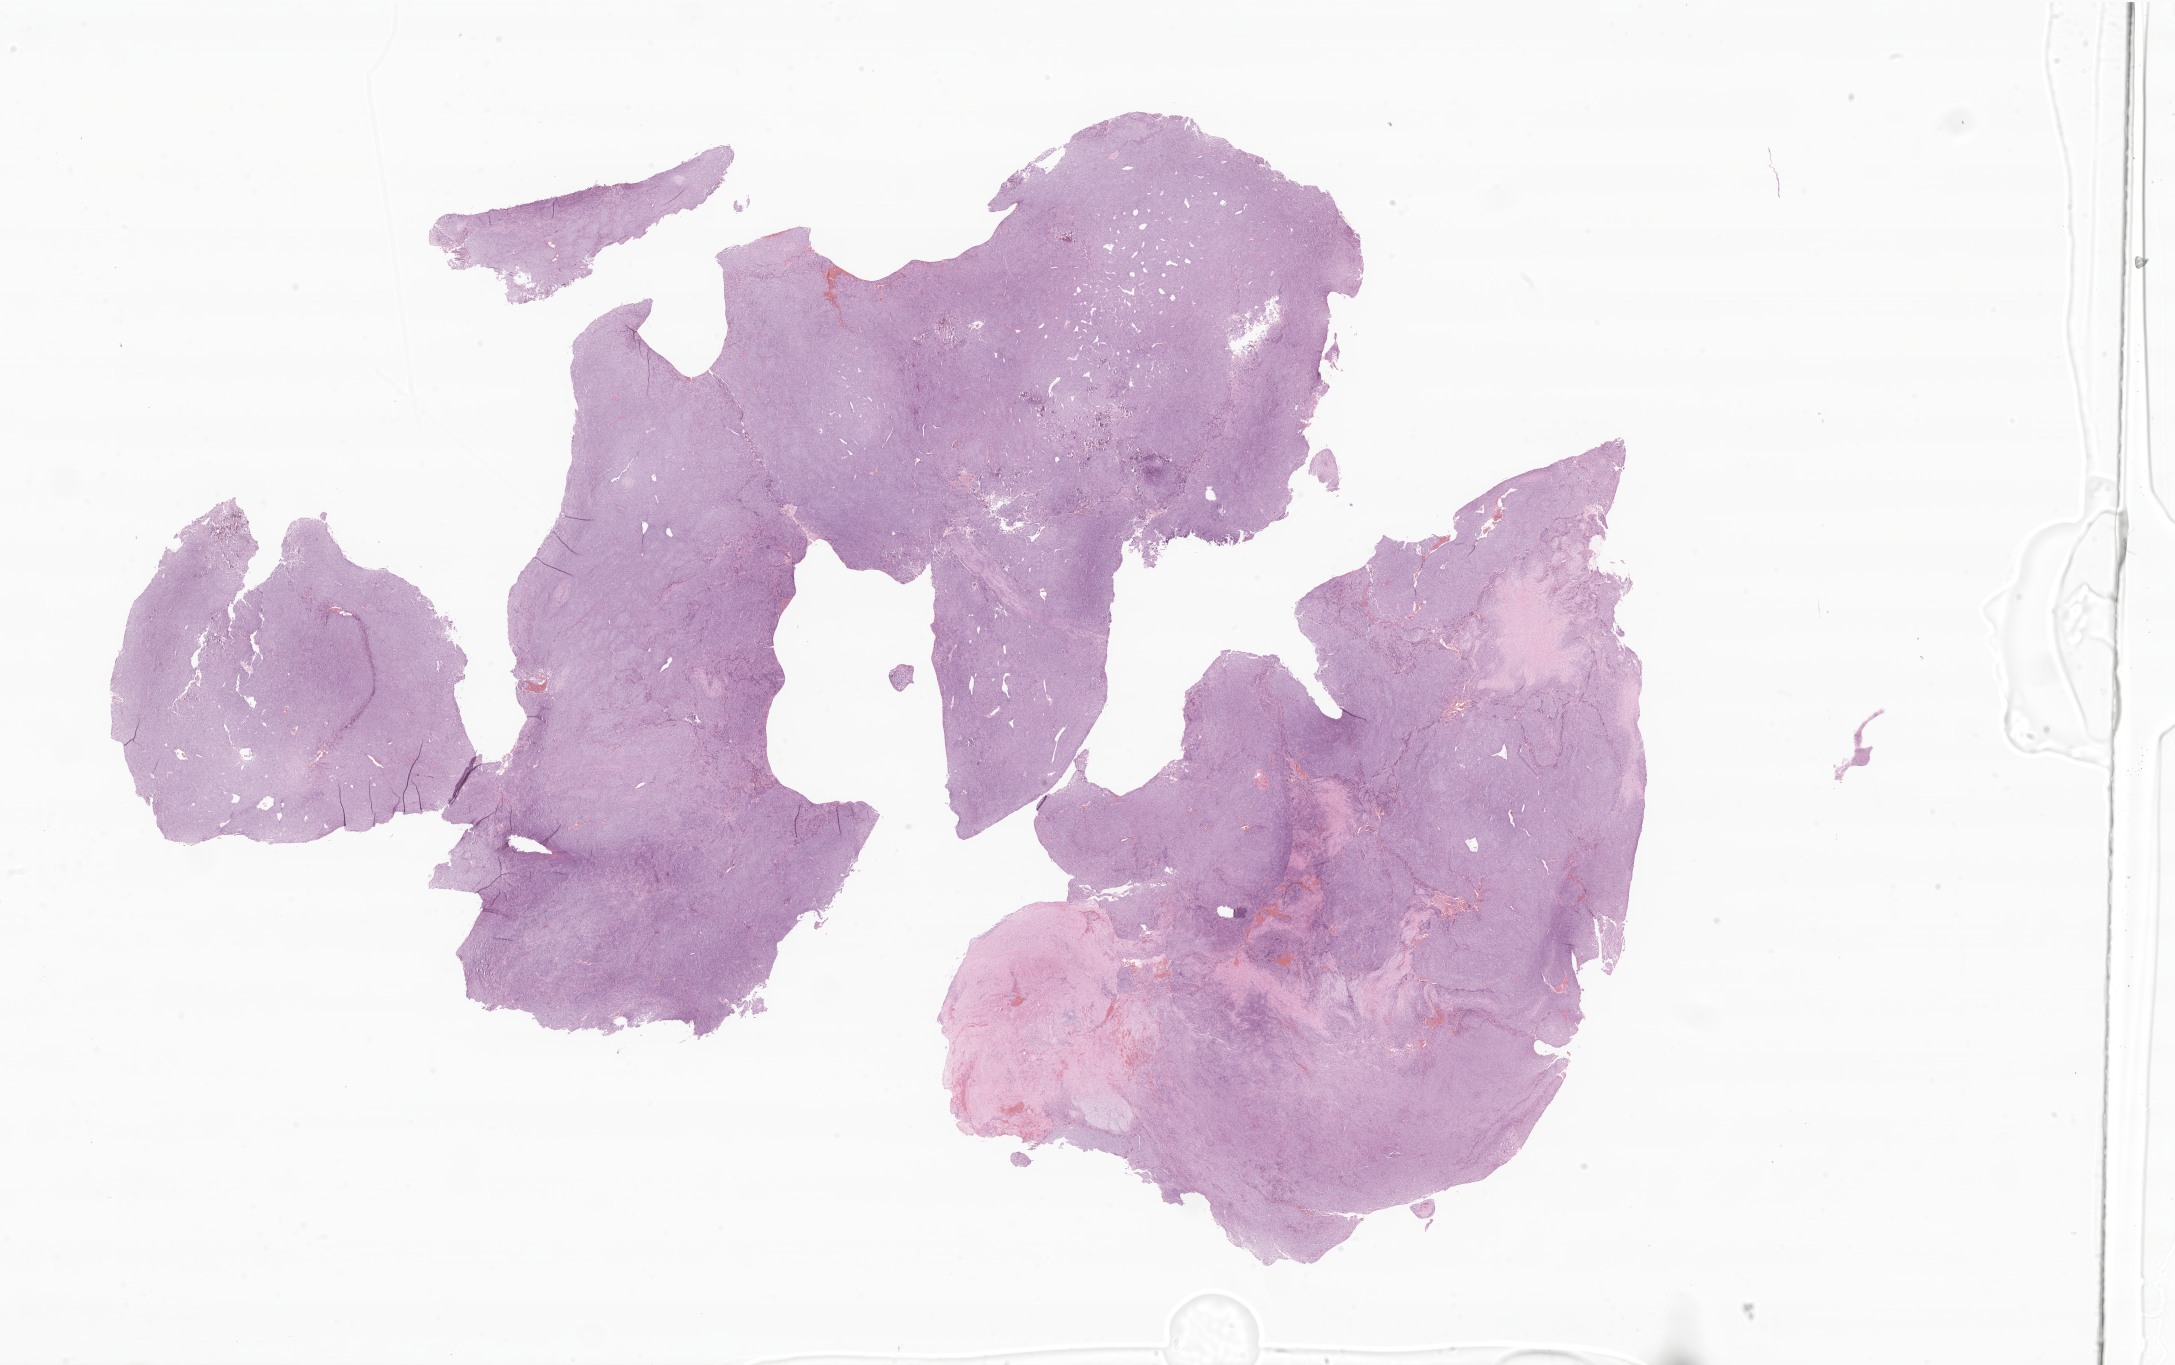
Haematoxylin and eosin whole-slide image of tumor tissue from the thorax — shown as a low-resolution overview of the whole scanned area (about 36.7 x 23.0 mm). FFPE section. Patient: male, age 114 months (9 years 6 months).
* recorded diagnosis: Synovial sarcoma, NOS